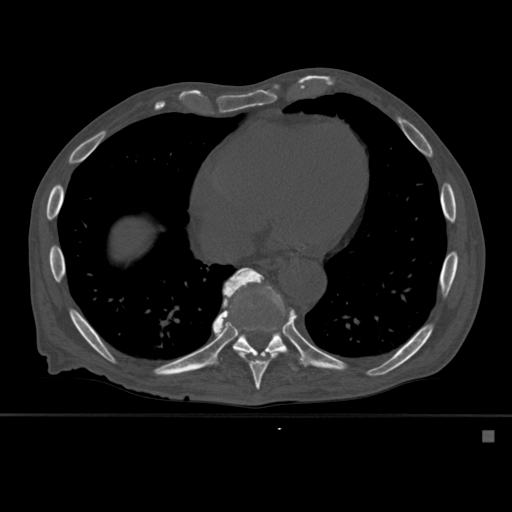
CT including the spine, one axial slice. Bone window (W 1800 / L 400 HU). 1.5 mm slice thickness. 512 × 512 image matrix. Patient: male, 78 years. From the clinical record (not read from this slice): primary cancer: prostate.
Outlined on this slice (semi-automatic segmentation, software-assisted and operator-edited):
- T10 vertebra: bounding box (x1, y1, x2, y2) in pixels: (218, 301, 302, 371)
- T9 vertebra: (219, 268, 297, 391)